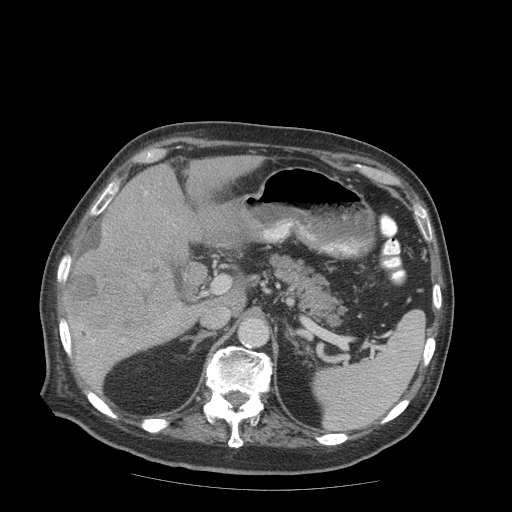
Contrast-enhanced abdominal CT (liver protocol), one axial slice. Slice 48 of 99 in the series (ordered by position). 140 kVp. Soft-tissue window (W 400 / L 40 HU). 2.5 mm slice thickness. 512 × 512 image matrix, field of view 420 × 420 mm. Case-level facts recorded for this patient, not image findings: diagnosis: hepatocellular carcinoma (patient treated with transarterial chemoembolisation; whether this scan precedes or follows treatment is not stated here); TNM stage (as recorded): Stage-IIIB; Child-Pugh class: A; tumour differentiation: well differentiated.
Structures marked on this image (semi-automatic segmentation, software-assisted and operator-edited):
- liver parenchyma outside the tumour (the mass and vessels are separate outlines, so this box may not span the whole liver): bounding box [x1, y1, x2, y2] px = [64, 156, 262, 387]
- mass: [64, 244, 172, 337]